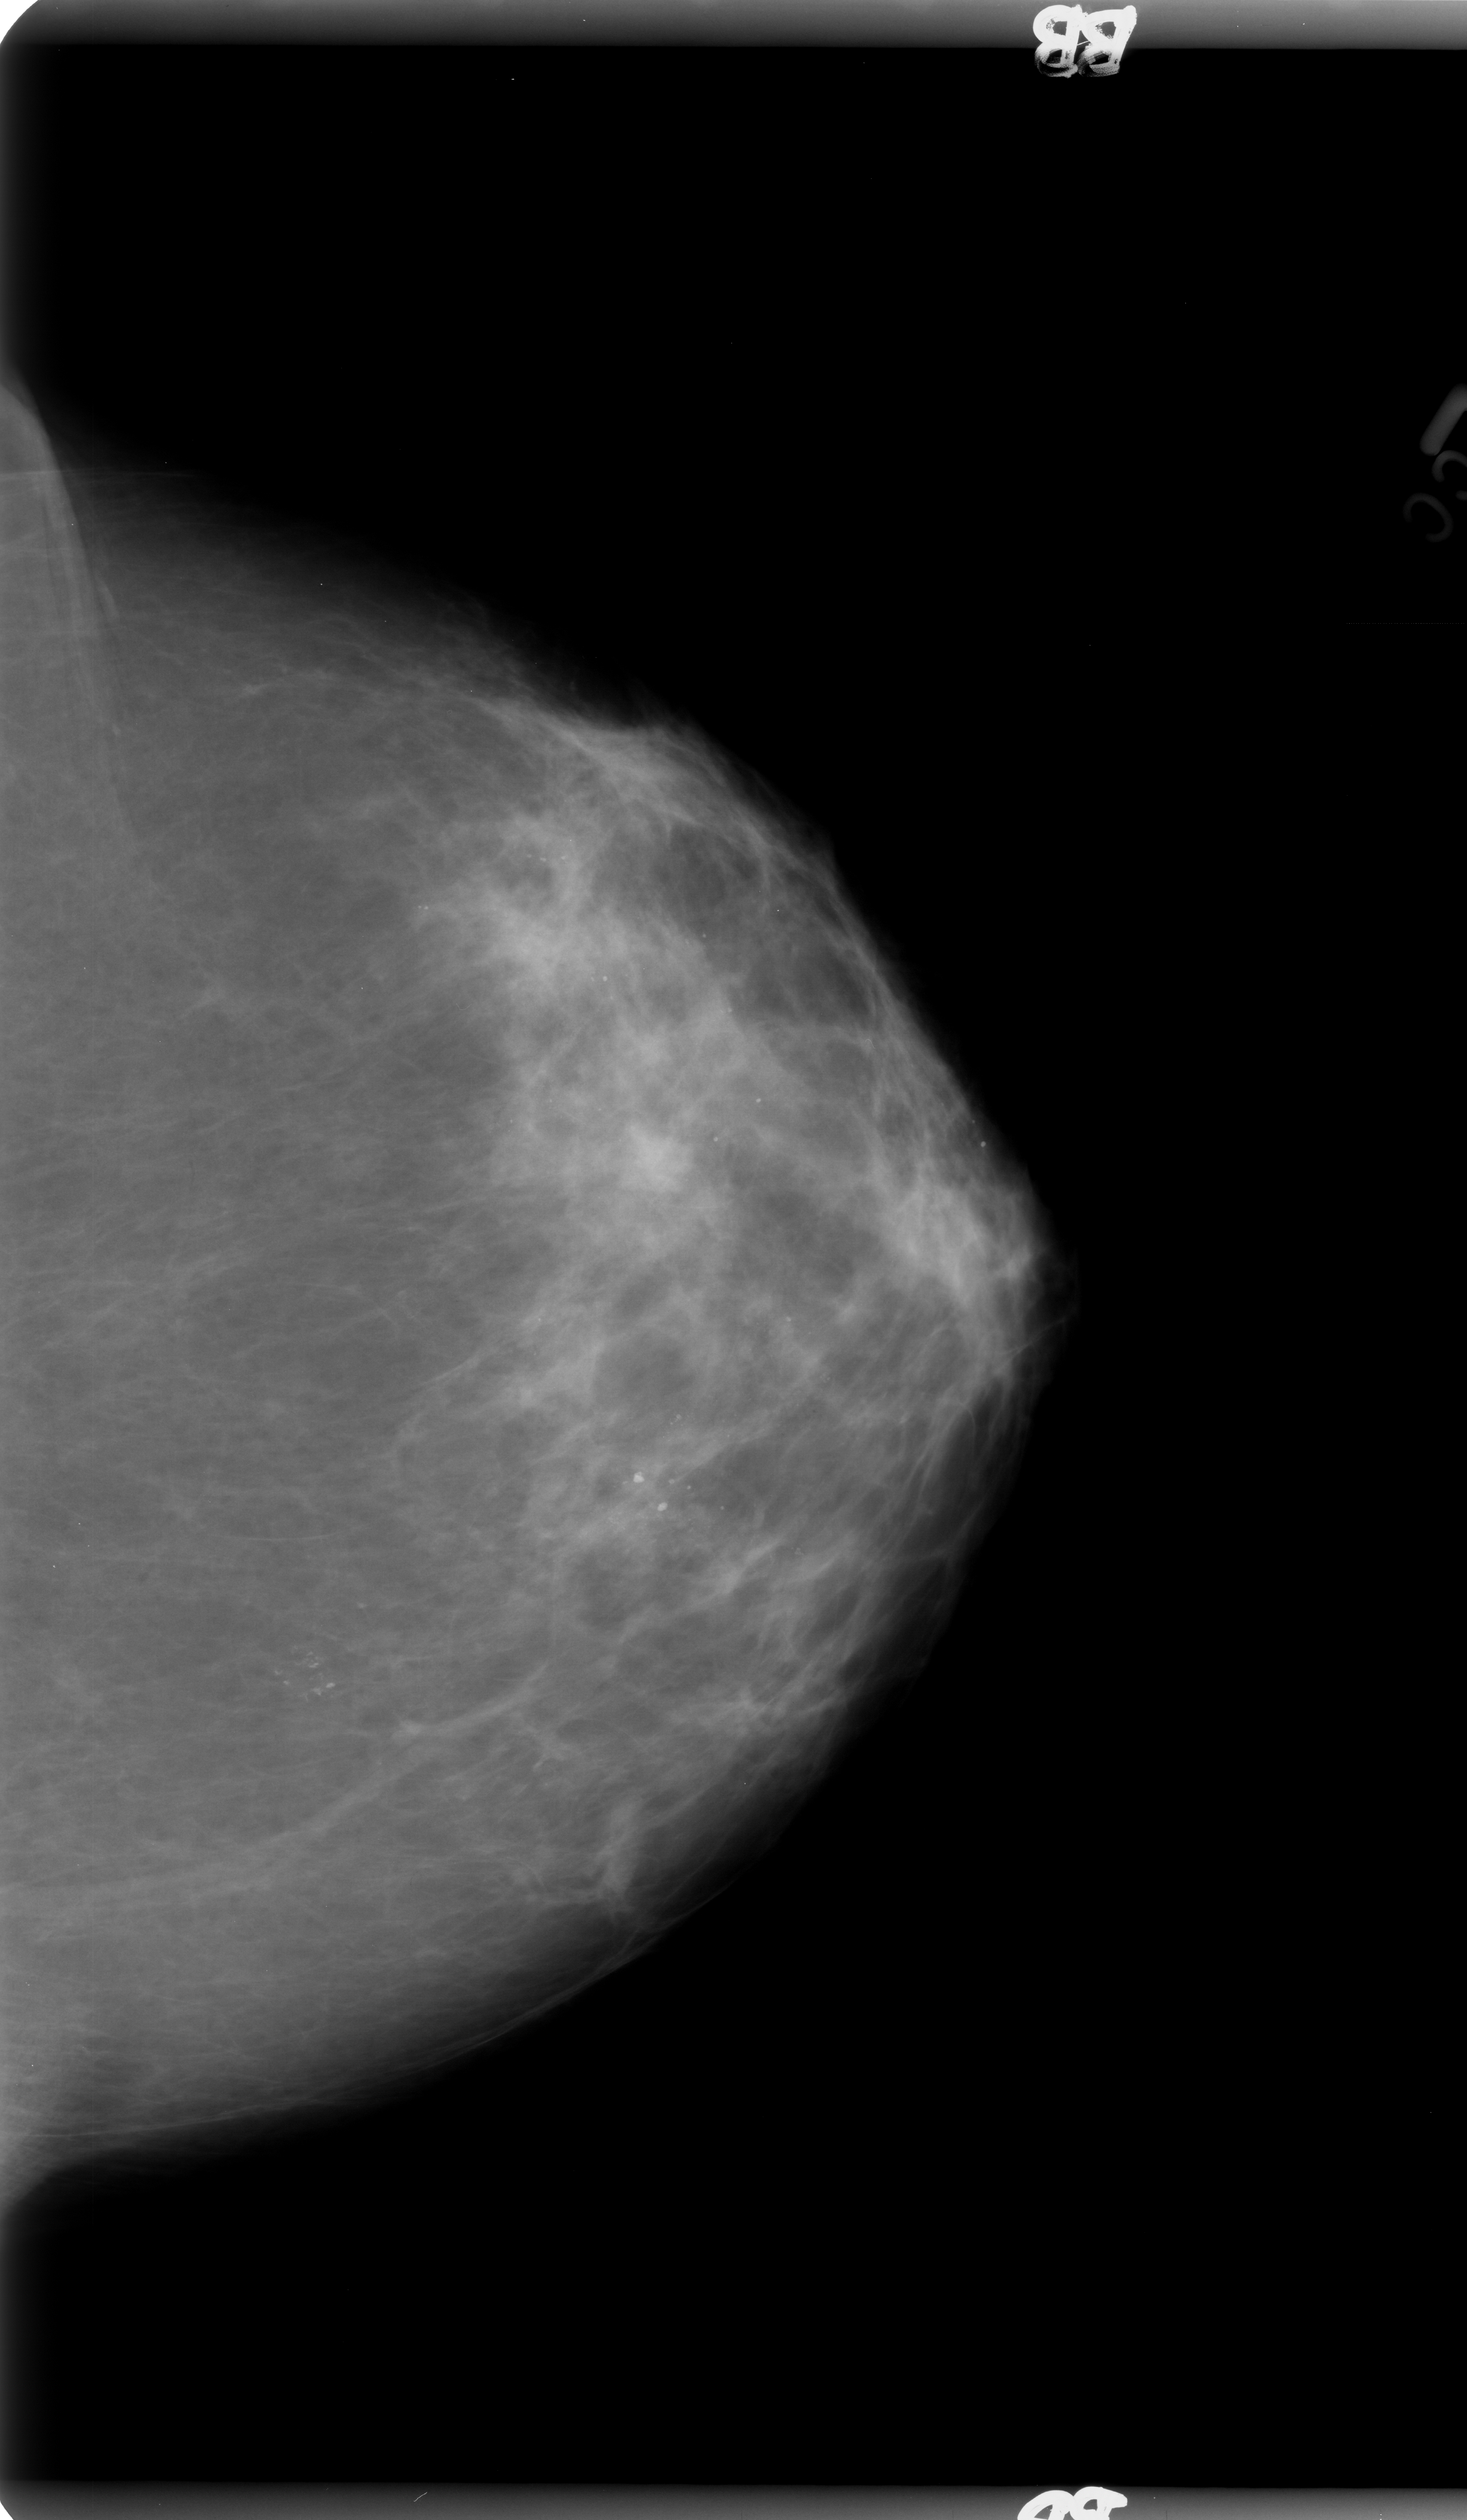
Digitized screen-film mammogram; left breast; CC view; breast composition: scattered fibroglandular densities (BI-RADS density category 2 of 4); 1467 × 2520 image matrix.
Marked abnormalities (boxes around the expert regions of interest):
- calcifications, morphology pleomorphic, distribution clustered; BI-RADS assessment category 4; pathology (as recorded): benign: bounding box (x1, y1, x2, y2) in pixels: (247, 1582, 385, 1736)